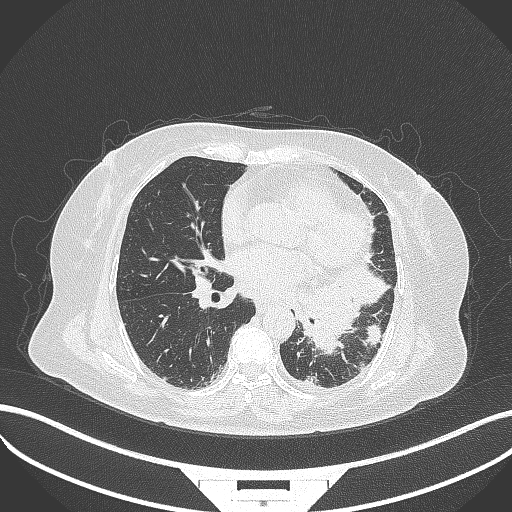
Chest CT, one axial slice. Slice 163 of 322 in the series (ordered by position). Reconstruction kernel B70f. 120 kVp. Lung window (W 1500 / L -600 HU). 512 × 512 image matrix. Female patient, age 69 years. Case-level facts recorded for this patient, not image findings: clinical TNM (as recorded): T2b N3 M1.
Annotated regions visible in this slice (rectangle marked by the reading radiologist):
- lung tumour (recorded histology: adenocarcinoma): bounding box <301,261,392,354> (left, top, right, bottom; pixels)